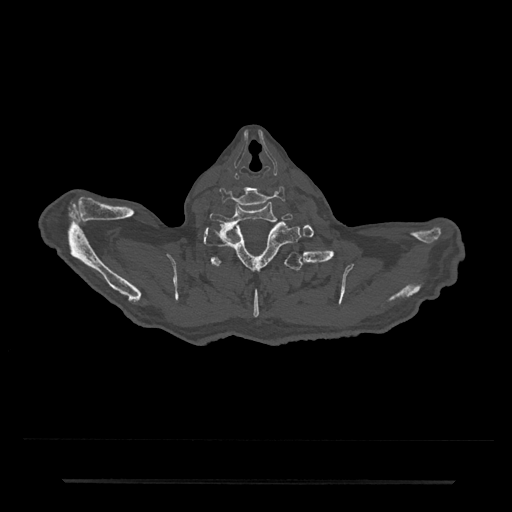
CT including the spine, one axial slice. Position 723 of 797 along the scan axis. Reconstruction kernel Br40s/3. Bone window (W 1800 / L 400 HU). 0.5 mm slice thickness. 512 × 512 image matrix, field of view 427 × 427 mm. Patient: male, 74 years. Case-level facts recorded for this patient, not image findings: primary cancer: prostate.
Annotated regions visible in this slice (semi-automatically segmented with operator editing):
- T1 vertebra: bounding box (x1, y1, x2, y2) in pixels: (203, 220, 301, 269)
- T2 vertebra: (210, 252, 314, 318)